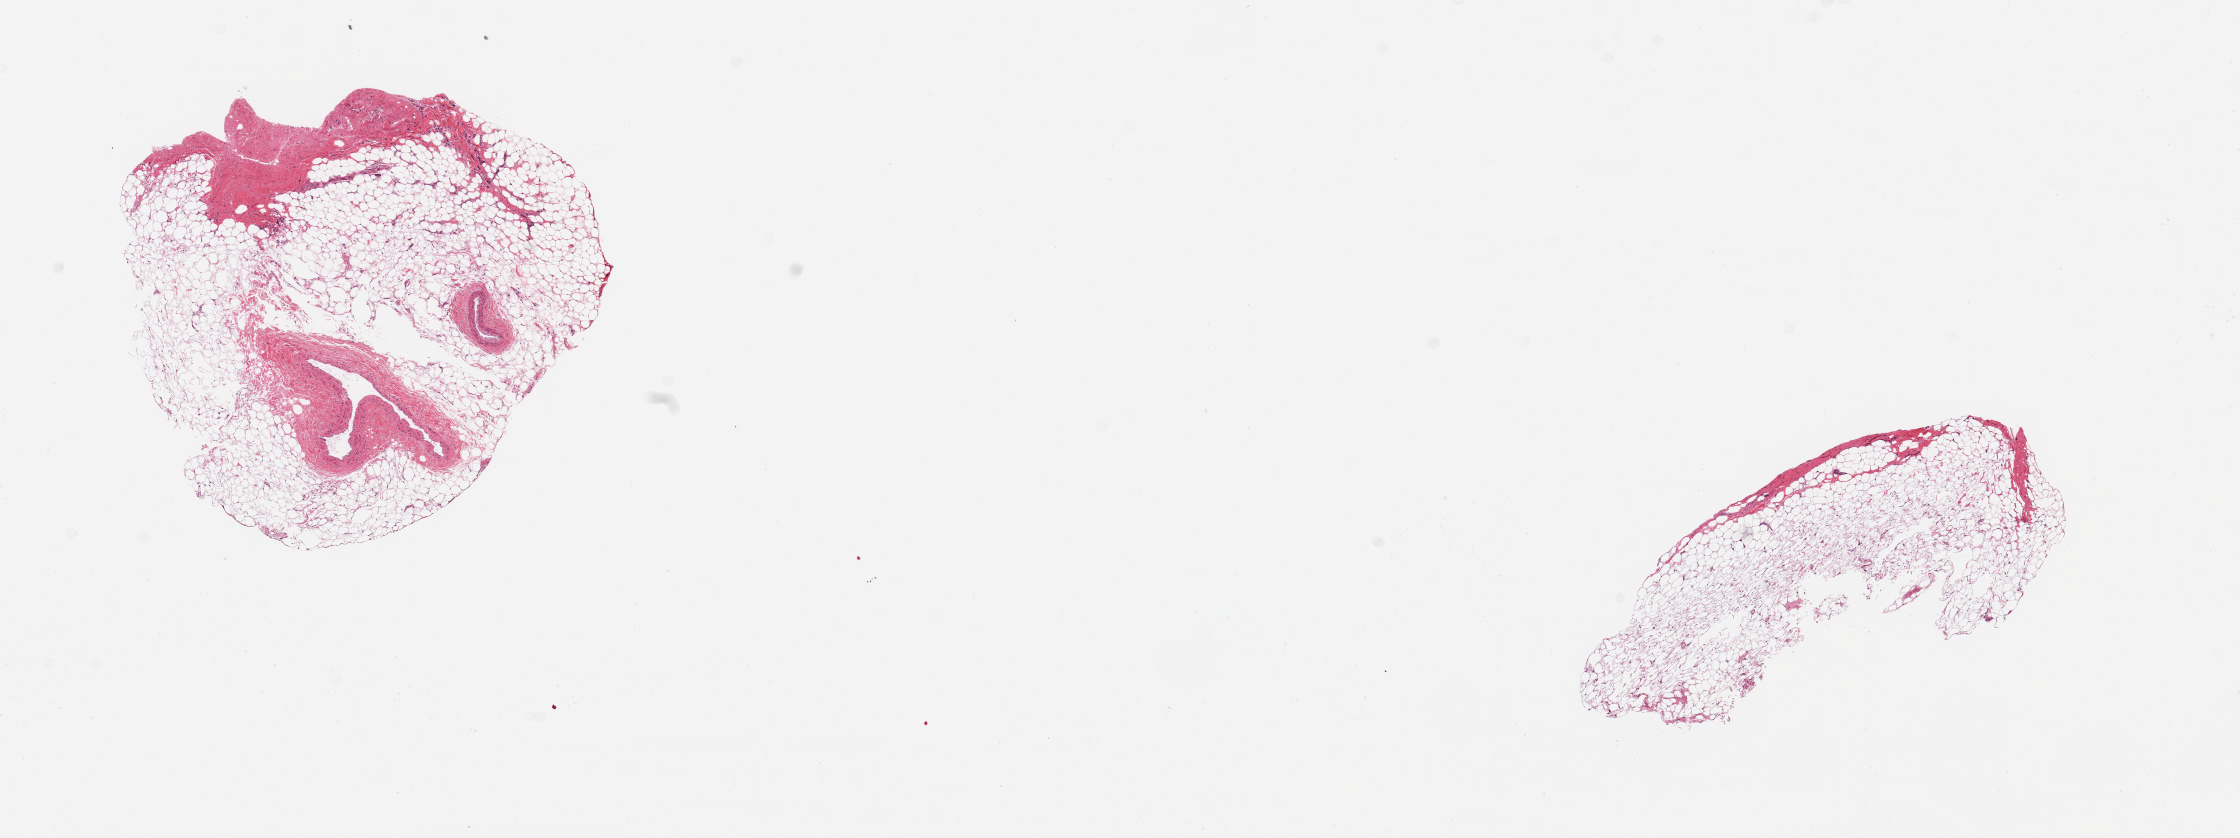
H&E whole-slide image — whole scanned area (about 17.7 x 6.6 mm, from a 20x scan) shown as a low-resolution overview. PAXgene-fixed, paraffin-embedded tissue. Sampled site (target tissue): coronary artery. Tissue donor sample. Donor: male.
Reviewer comment on this tissue sample: 2 pieces; 1 all fat; other 90% fibrofatty tissue with small vein & very small artery.